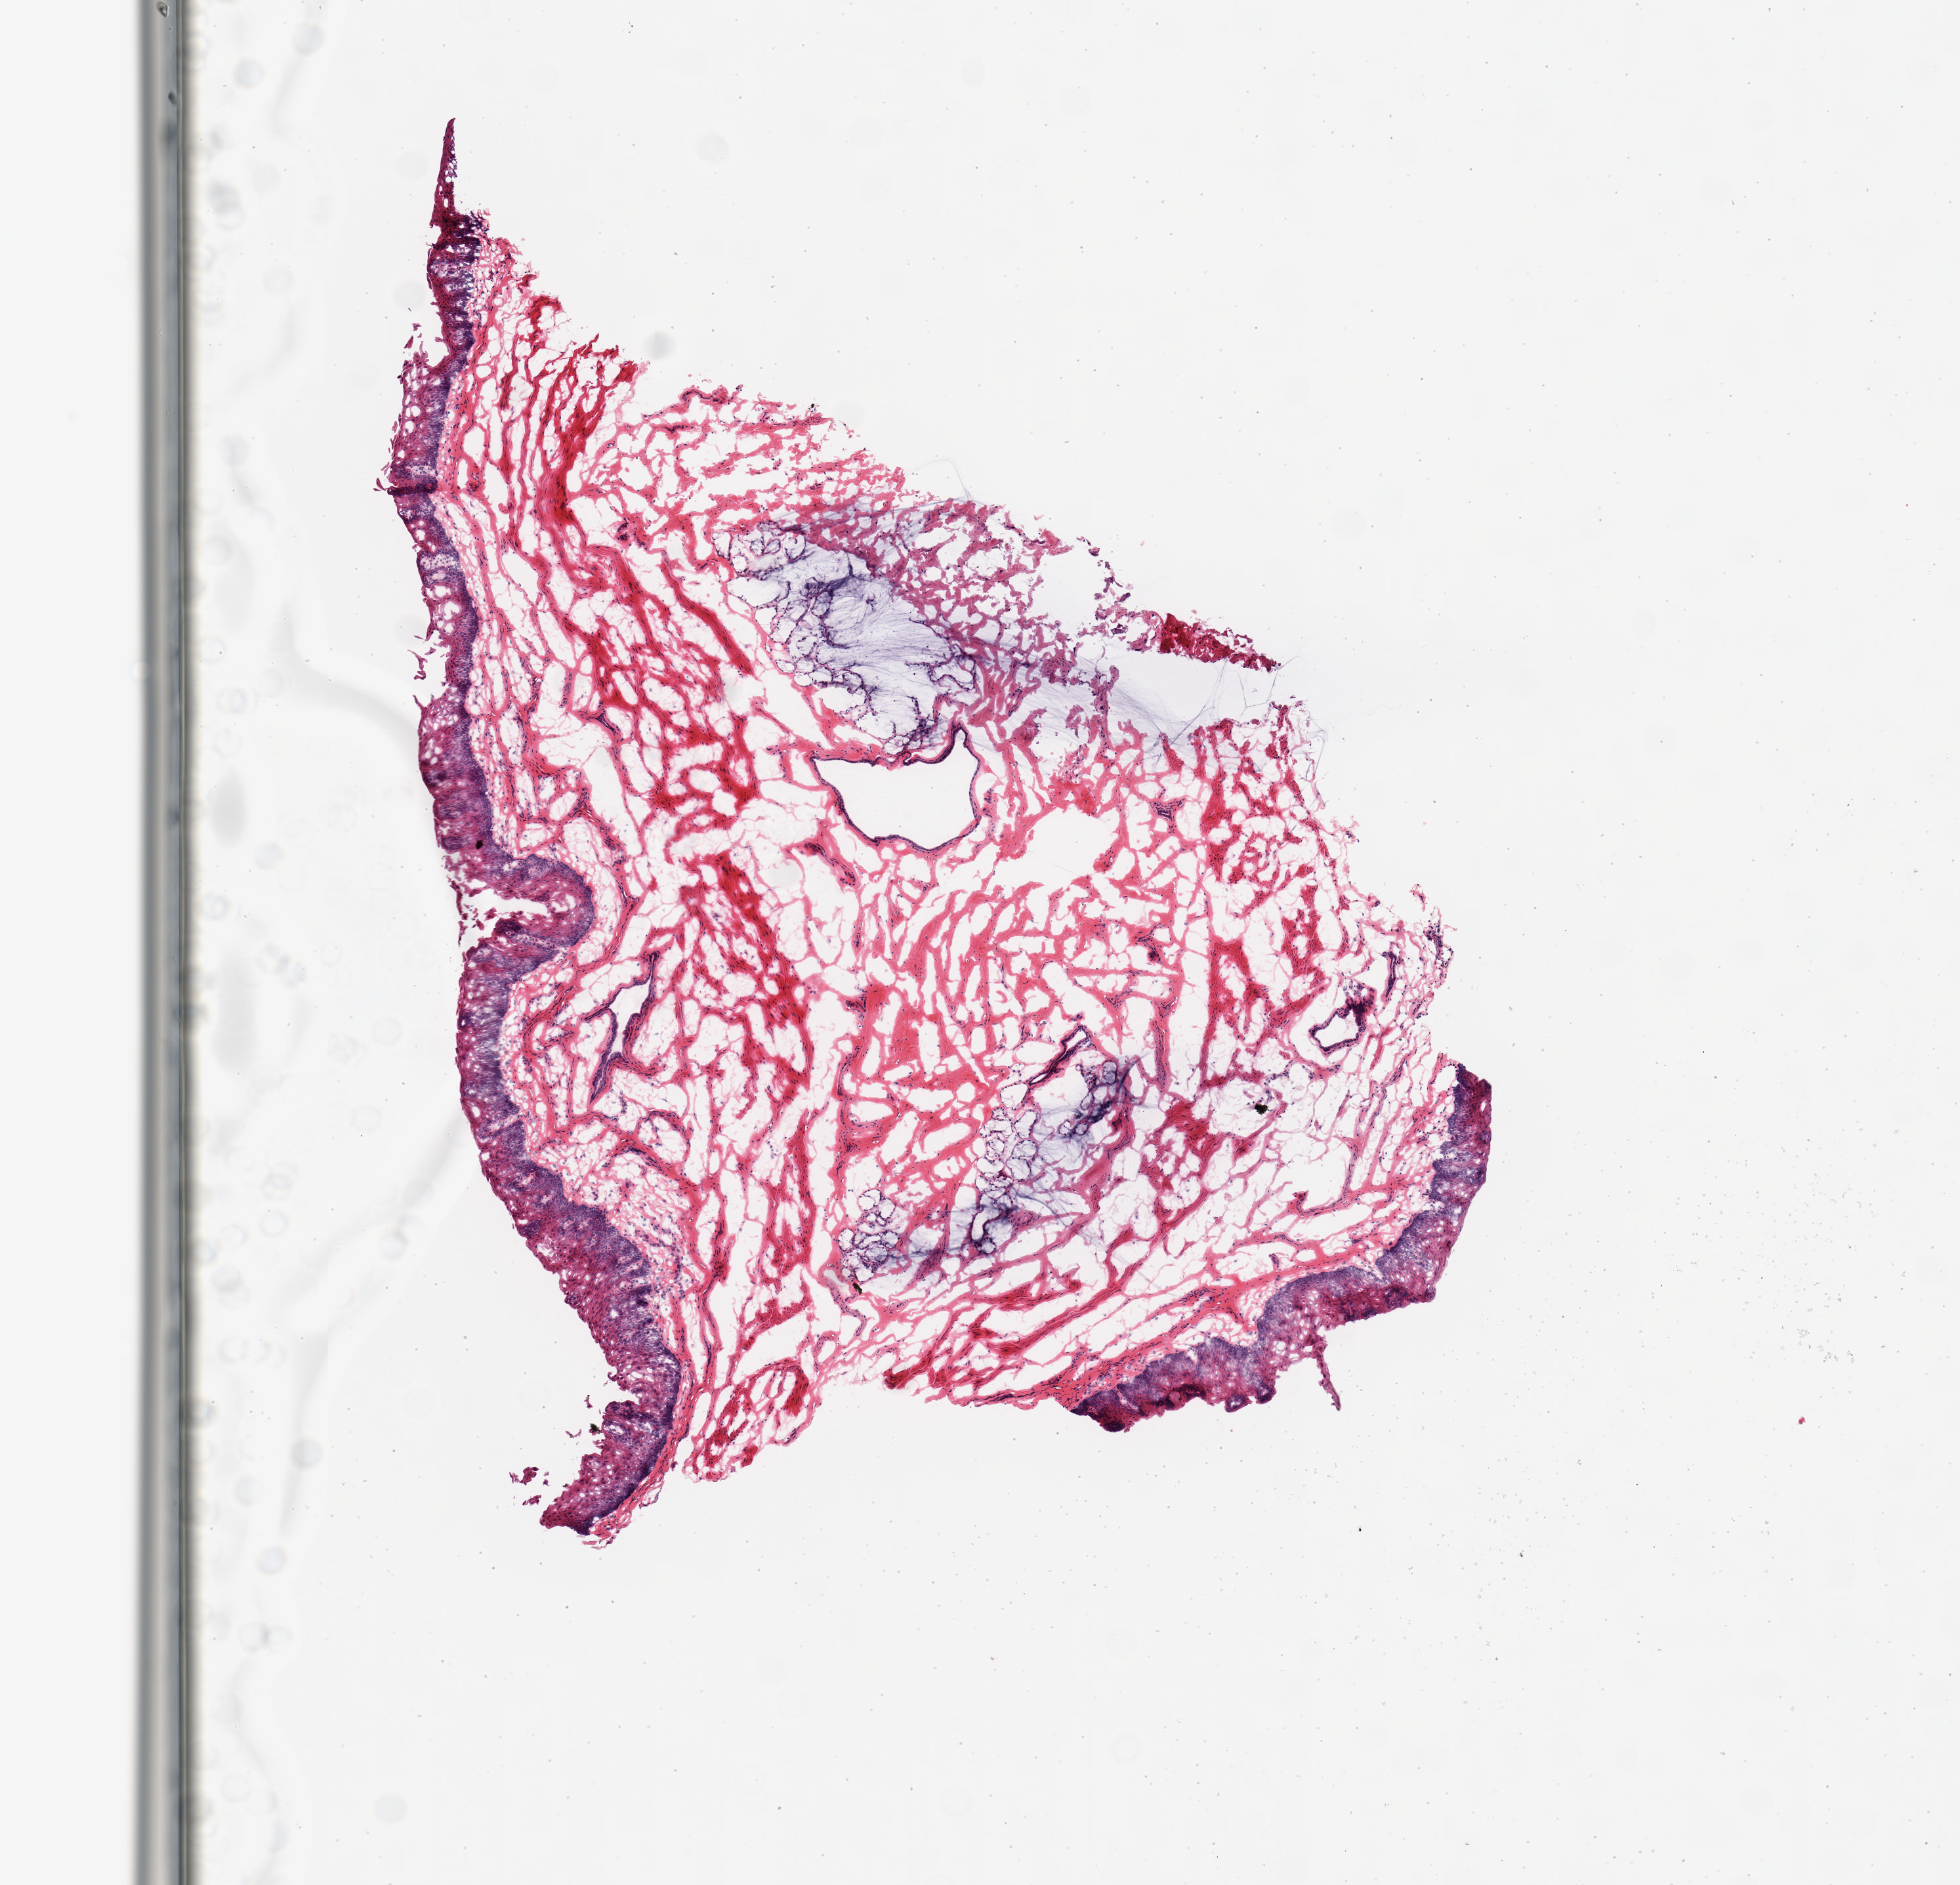
Whole-slide image, H&E stain — a low-resolution overview of the entire scanned area, about 5.9 x 5.7 mm; frozen section (dry ice); target tissue: esophageal mucous membrane; donor tissue sample.
Reviewer comment on this tissue sample: 1 piece; comparable to PAXgene sample.